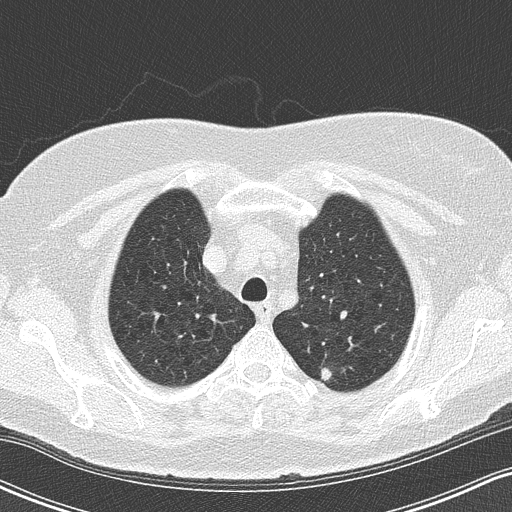
Axial slice from a low-dose chest CT screening exam; third annual screen; lung window (W 1500 / L -600 HU); slice 24 of 155 in the series; 512 × 512 image matrix. Female, age 65 years at enrolment. Former smoker at enrolment.
Lesion marked by an expert reader, bounding box <308,352,349,394> (left, top, right, bottom; pixels). The exam's reader record, not a measurement of the box and not confirmed to be the same lesion: non-calcified nodule or mass ≥4 mm, left upper lobe, 8 × 6 mm, pre-existing on the prior screen: yes. Official screen result: positive, no significant change: stable abnormalities potentially related to lung cancer, unchanged since the prior screening exam. Lung cancer was diagnosed 103 days after this screen: adenocarcinoma, NOS, left upper lobe, moderately differentiated (G2), stage IA (AJCC 6th edition), 8 mm at pathology.